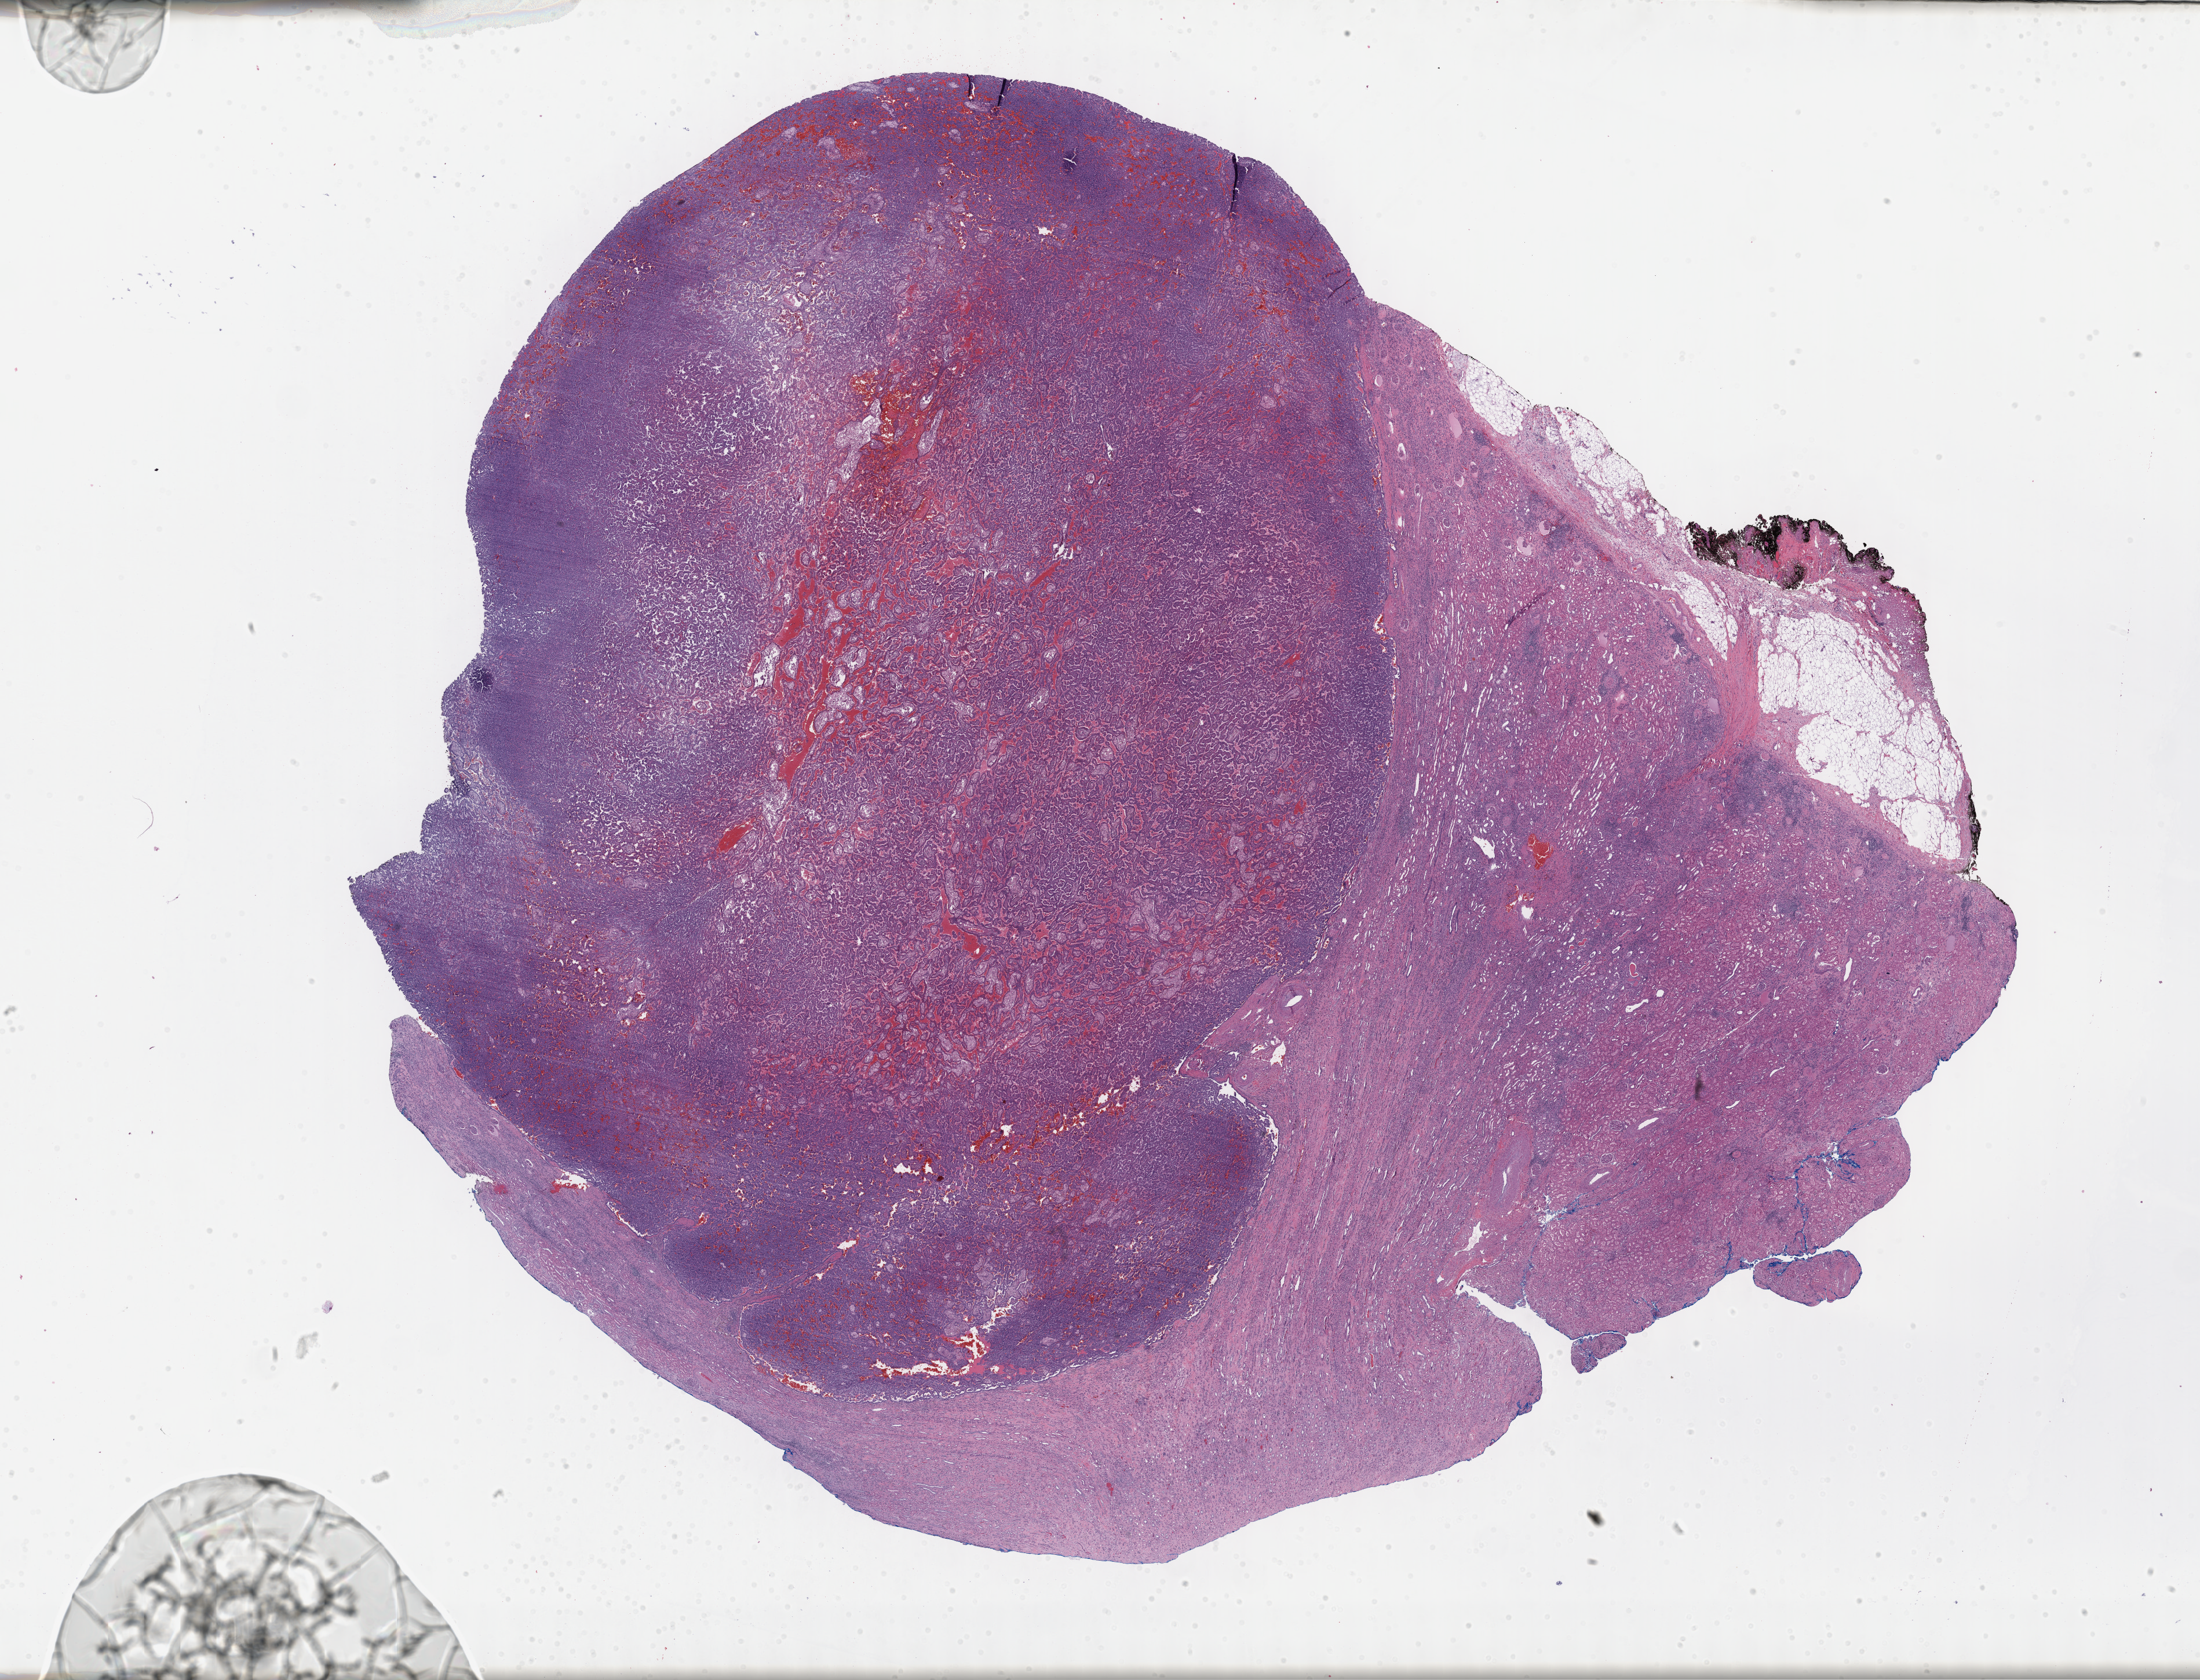
Digitized H&E-stained tissue section (whole slide) — low-resolution overview of the scanned area, about 30.7 x 23.5 mm (from a 40x scan); formalin-fixed paraffin-embedded (FFPE) diagnostic section; primary tumour sample from the kidney. Male, age 66 years at initial diagnosis.
• AJCC pathologic stage: I
• histologic diagnosis: Papillary adenocarcinoma, NOS
• TNM: T1a NX MX